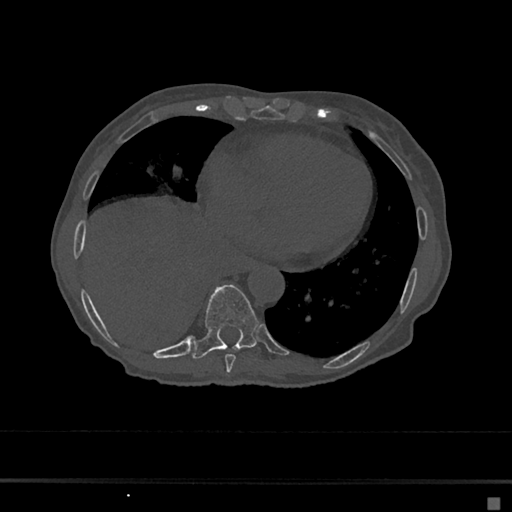
CT including the spine, one axial slice. Position 286 of 797 along the scan axis. Reconstruction kernel Br40s/3. 120 kVp. Bone window (W 1800 / L 400 HU). 0.5 mm slice thickness. 512 × 512 image matrix, field of view 360 × 360 mm. Patient: female, 68 years. Case-level facts recorded for this patient, not image findings: primary cancer: renal.
Structures marked on this image (semi-automatic segmentation, software-assisted and operator-edited):
- T8 vertebra: bounding box [x1, y1, x2, y2] px = [225, 354, 236, 373]
- T9 vertebra: [192, 284, 259, 359]